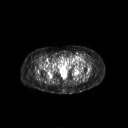
FDG PET of an extremity soft-tissue mass (from a PET/CT study), one axial slice. Slice 51 of 267 in the series (ordered by position). 128 × 128 image matrix, field of view 700 × 700 mm. Patient: female, 47 years. Case-level facts recorded for this patient, not image findings: histological type: myxofibrosarcoma; grade: intermediate; site of the primary tumour: left thigh.
Annotated regions visible in this slice (expert contour drawn on MRI and transferred to this co-registered scan by the dataset authors):
- gross tumour volume including surrounding oedema: bounding box [x1, y1, x2, y2] px = [66, 56, 82, 63]